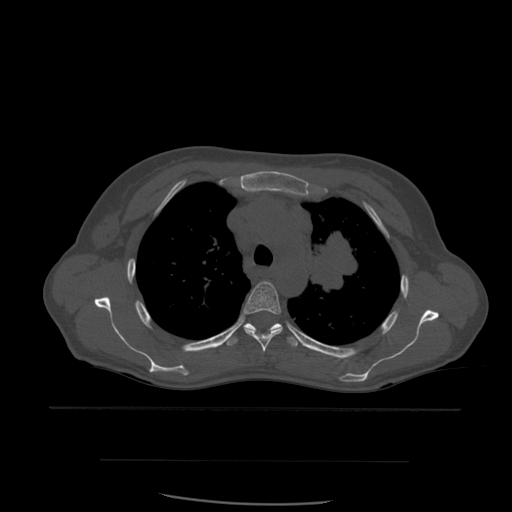
CT including the spine, one axial slice; slice 422 of 574 in the series (ordered by position); bone window (W 1800 / L 400 HU); 1.25 mm slice thickness; 512 × 512 image matrix, field of view 392 × 392 mm. Patient age 48 years. Case-level facts recorded for this patient, not image findings: primary cancer: lung; vertebrae with lytic lesions (as recorded): T11.
Structures marked on this image (semi-automatically segmented with operator editing):
- T4 vertebra: bounding box [x1, y1, x2, y2] px = [243, 281, 283, 353]
- T5 vertebra: [225, 323, 302, 348]